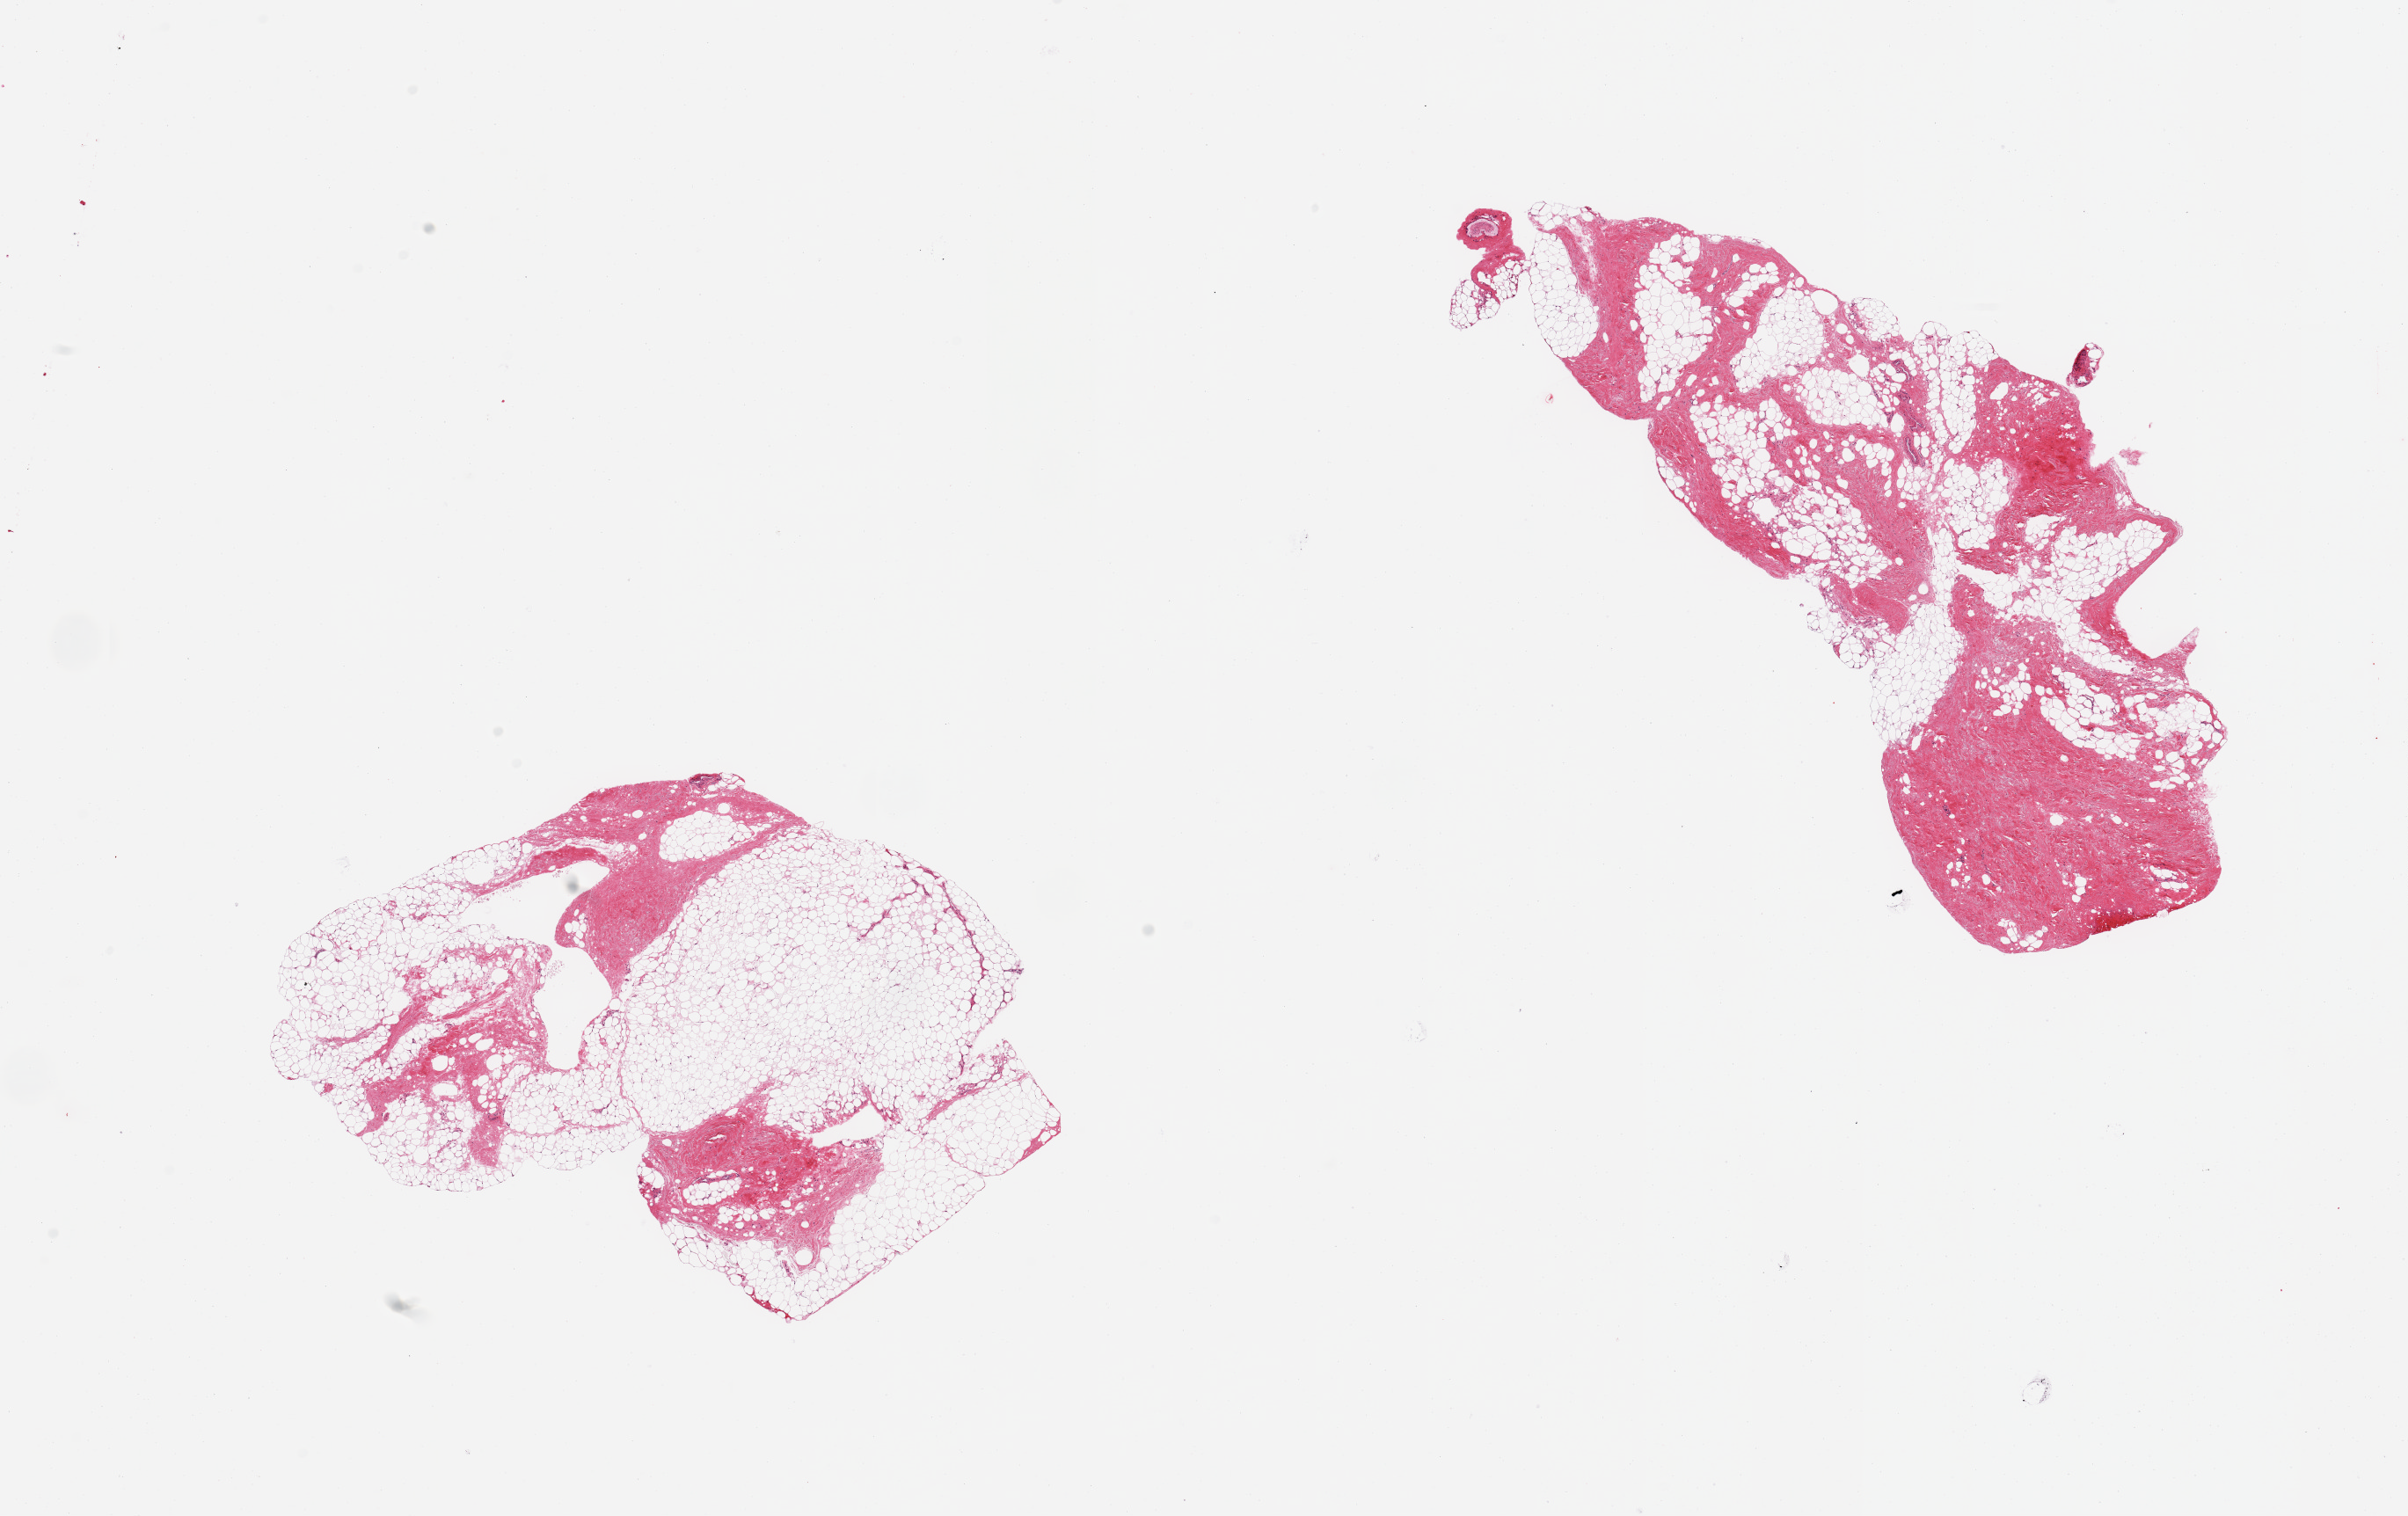
H&E whole-slide image, brightfield, a low-resolution overview of the entire scanned area, about 21.7 x 13.6 mm (acquisition: 20x scan); PAXgene-fixed, paraffin-embedded tissue; target tissue: breast; tissue donor sample. Donor sex: male.
* pathologist's review note for this sample: 2 pieces, gynecomastoid stromal hyperplasia